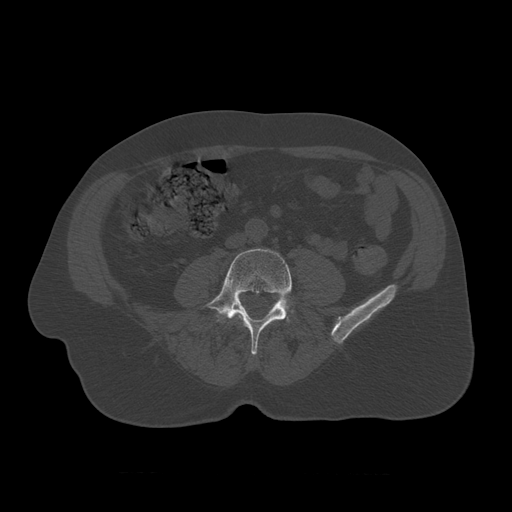
CT including the spine, one axial slice; slice 277 of 450 in the series (ordered by position); 120 kVp; bone window (W 1800 / L 400 HU); 512 × 512 image matrix, field of view 405 × 405 mm. Patient age 75 years. From the clinical record (not read from this slice): primary cancer: prostate.
Structures marked on this image (semi-automatic segmentation, software-assisted and operator-edited):
- L3 vertebra: bounding box [x1, y1, x2, y2] px = [235, 316, 240, 322]
- L4 vertebra: [204, 249, 292, 356]
- L5 vertebra: [275, 299, 293, 313]